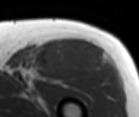
MRI of an extremity soft-tissue mass, one axial slice. Slice 70 of 86 in the series (ordered by position). MR volume resampled by the dataset authors to the PET/CT grid (not the native acquisition matrix). 3.27 mm slice thickness. 139 × 117 image matrix, field of view 136 × 114 mm. Male patient. Case-level facts recorded for this patient, not image findings: histological type: extraskeletal osteosarcoma; grade: high; site of the primary tumour: thigh.
Annotated regions visible in this slice (expert contour drawn on MRI and transferred to this co-registered scan by the dataset authors):
- gross tumour volume (mass): bounding box (x1, y1, x2, y2) in pixels: (42, 41, 107, 76)